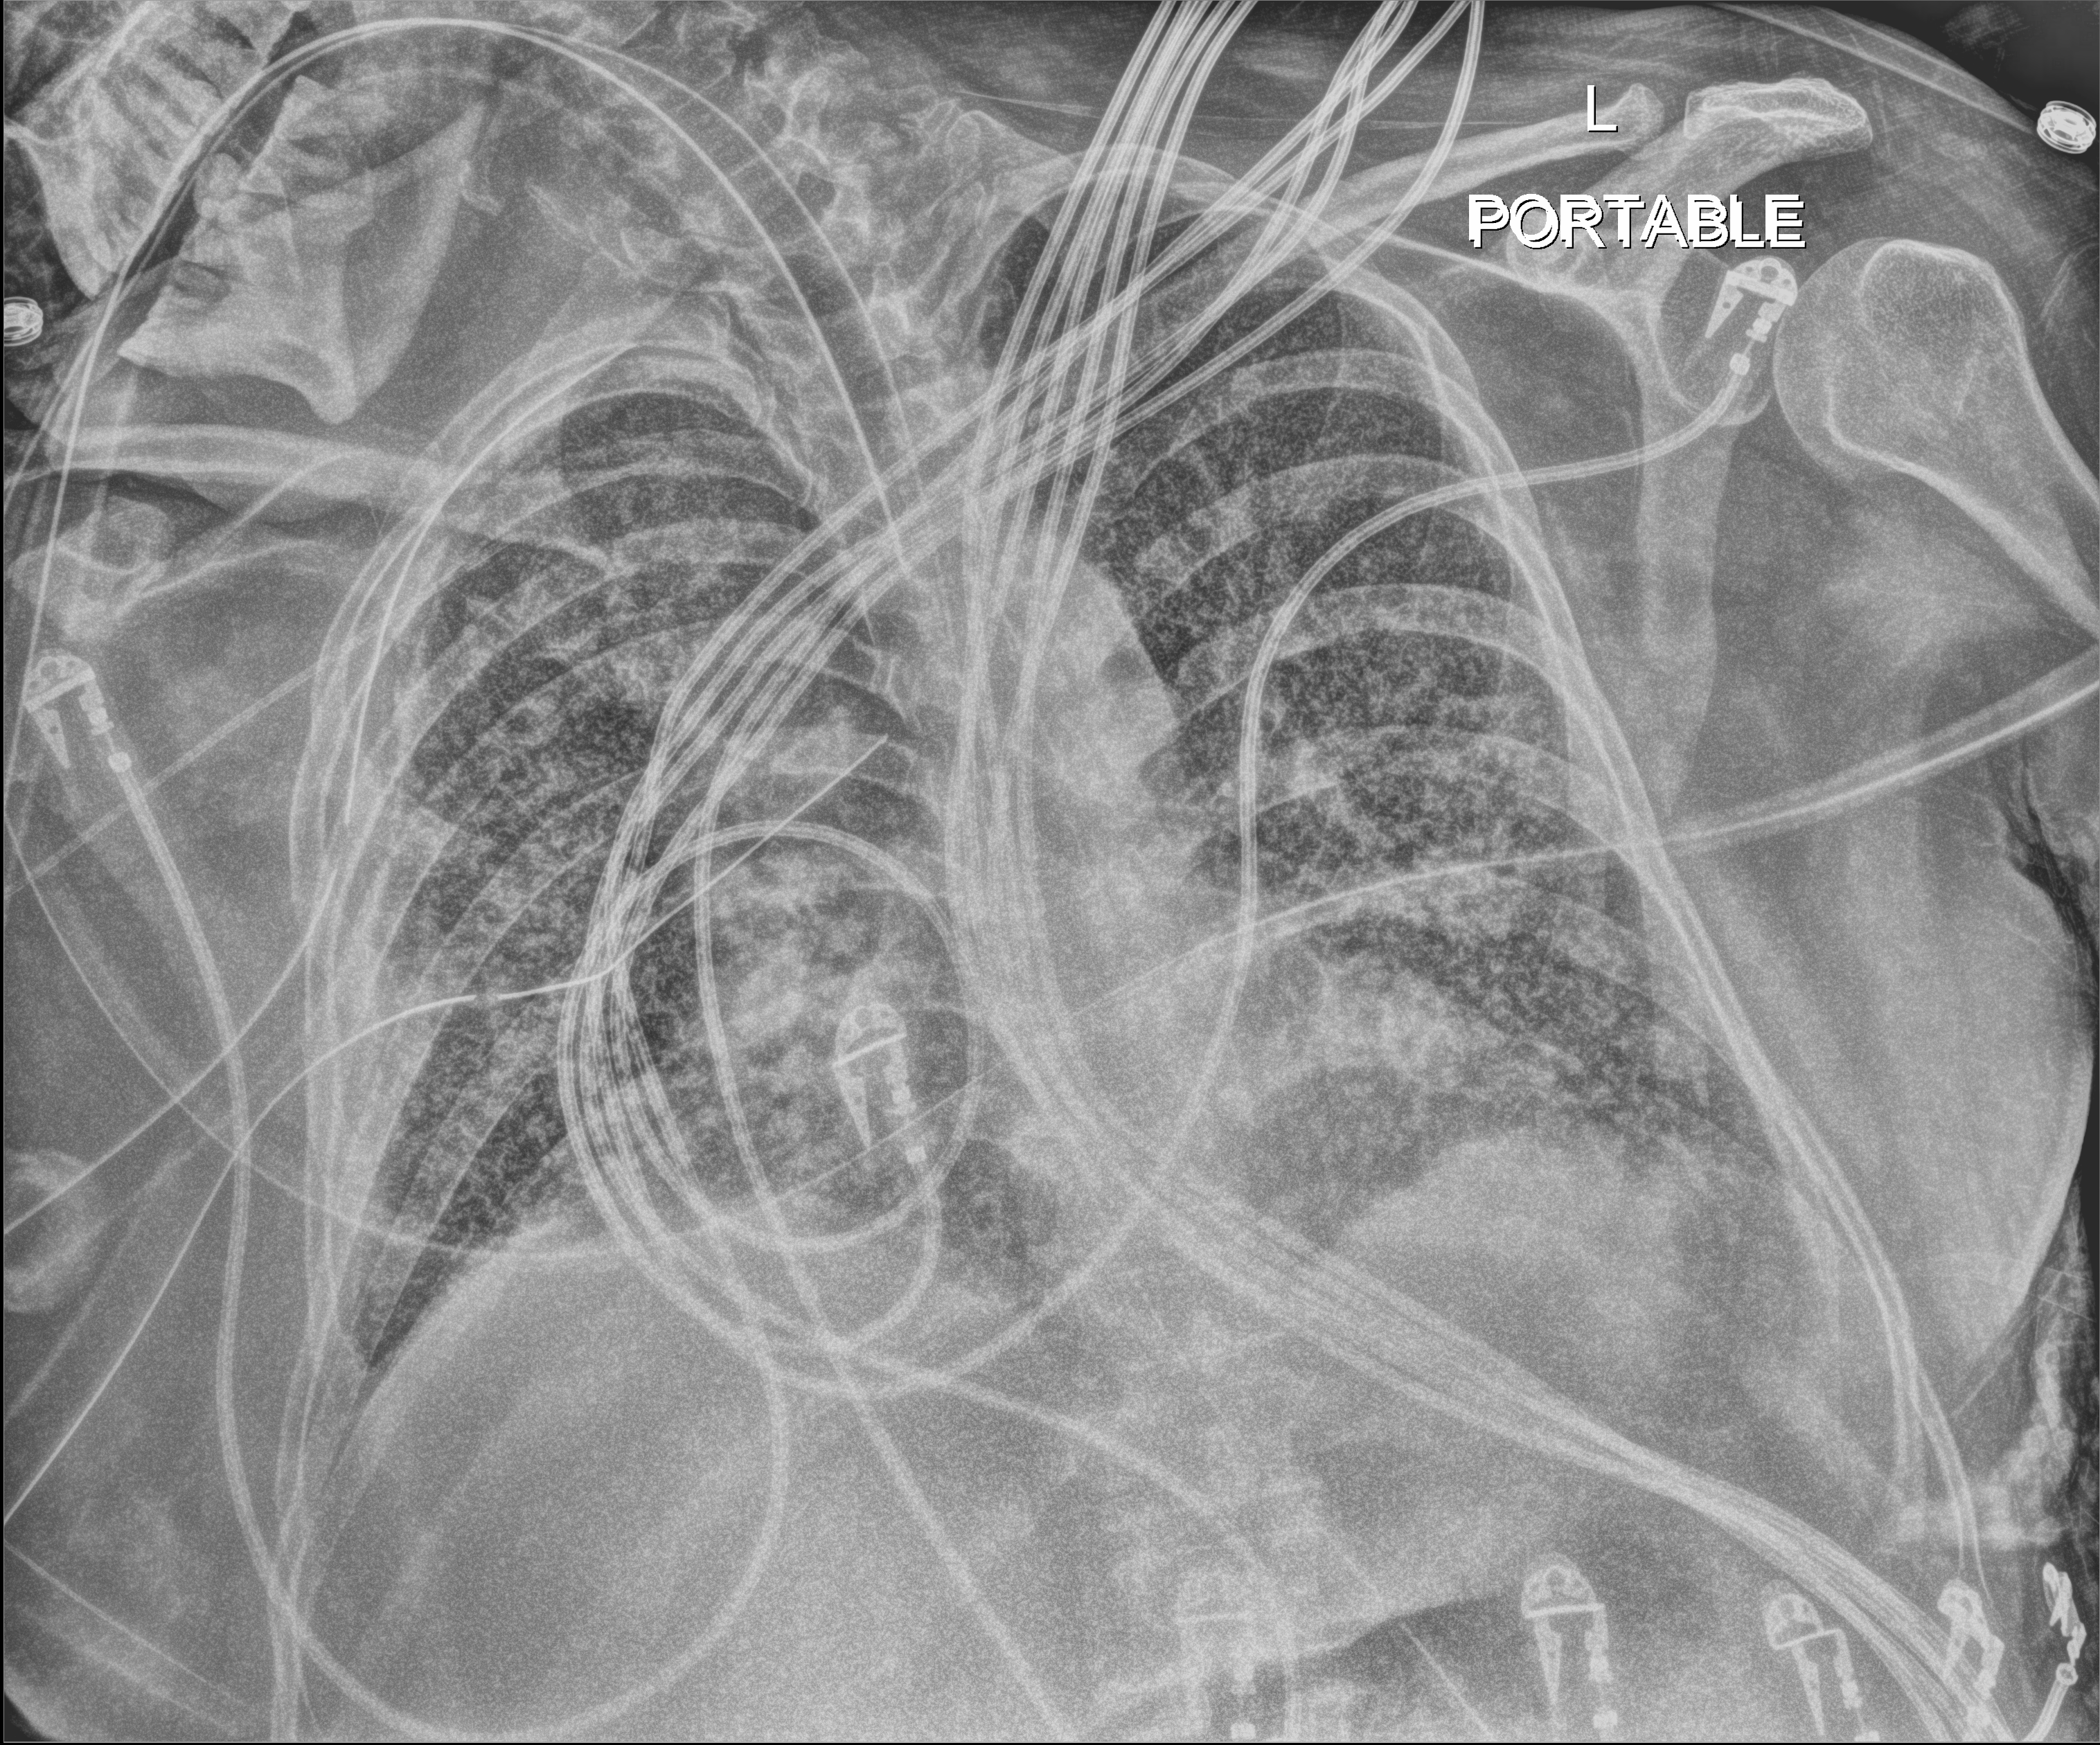
Chest X-ray; anteroposterior (AP) projection. Adult patient hospitalised with COVID-19, age 18–59 years.
Hospital-stay facts (about this admission, not read from this image; timing relative to this image not recorded): admitted to intensive care during this hospital stay: yes; length of hospital stay: 48 days.